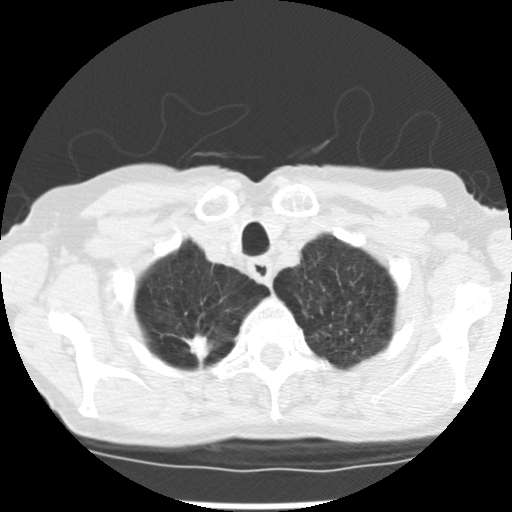
Low-dose screening chest CT, axial slice. Baseline screening round. Lung window (W 1500 / L -600 HU). 2.5 mm slice thickness. Slice 24 of 265 in the series. 512 × 512 image matrix. Female participant, aged 72 years at enrolment.
Expert reader's lesion annotation, bounding box (x1, y1, x2, y2) in pixels: (169, 316, 231, 362). The screening reader recorded 3 non-calcified nodules or masses ≥4 mm on this exam (right upper lobe, left upper lobe, left lower lobe); which of them this box marks is not recorded. Official screen result: positive, change unspecified: nodule(s) >= 4 mm or enlarging nodule(s), mass(es), or other non-specific abnormalities suspicious for lung cancer. Participant outcome: lung cancer diagnosed 50 days after this screen — adenocarcinoma, NOS, right upper lobe, moderately differentiated (G2), stage IB (AJCC 6th edition), 22 mm at pathology.